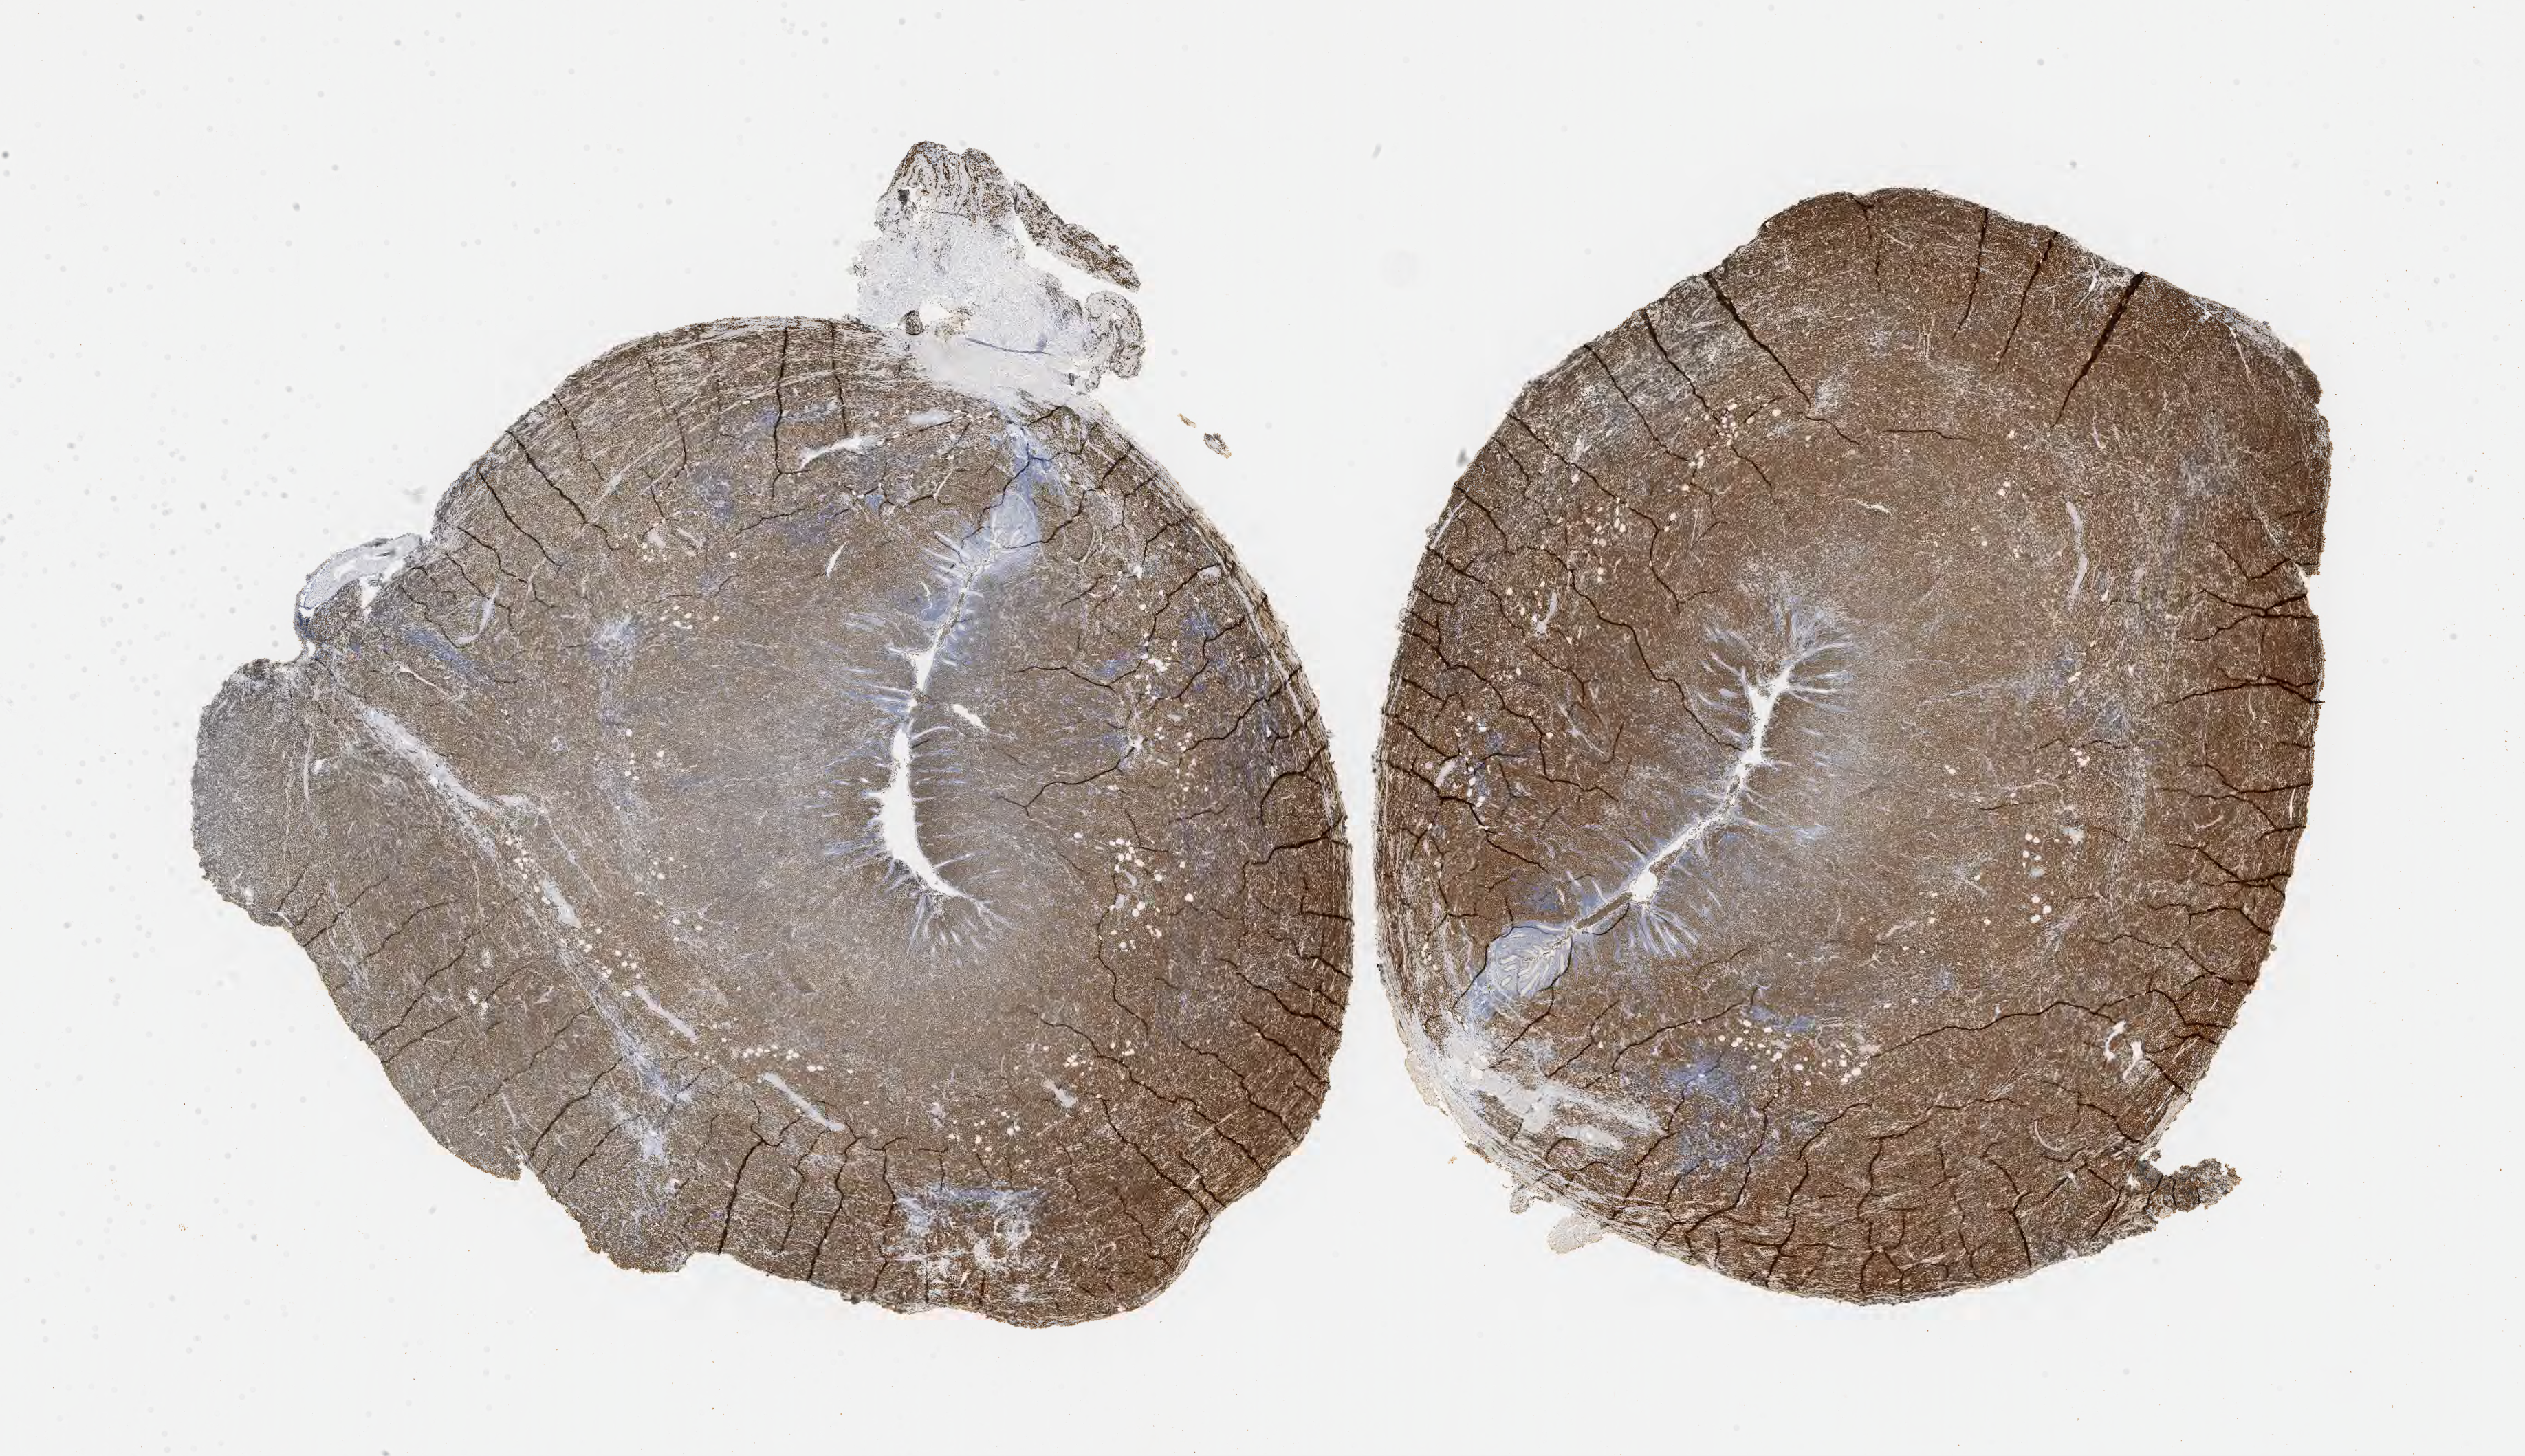
Whole-slide image, immunohistochemical stain for BCL6 — a low-resolution overview of the entire scanned area, about 29.7 x 17.1 mm, tumor tissue. Patient male; aged 63.
• histologic diagnosis: Diffuse large B-cell lymphoma, NOS